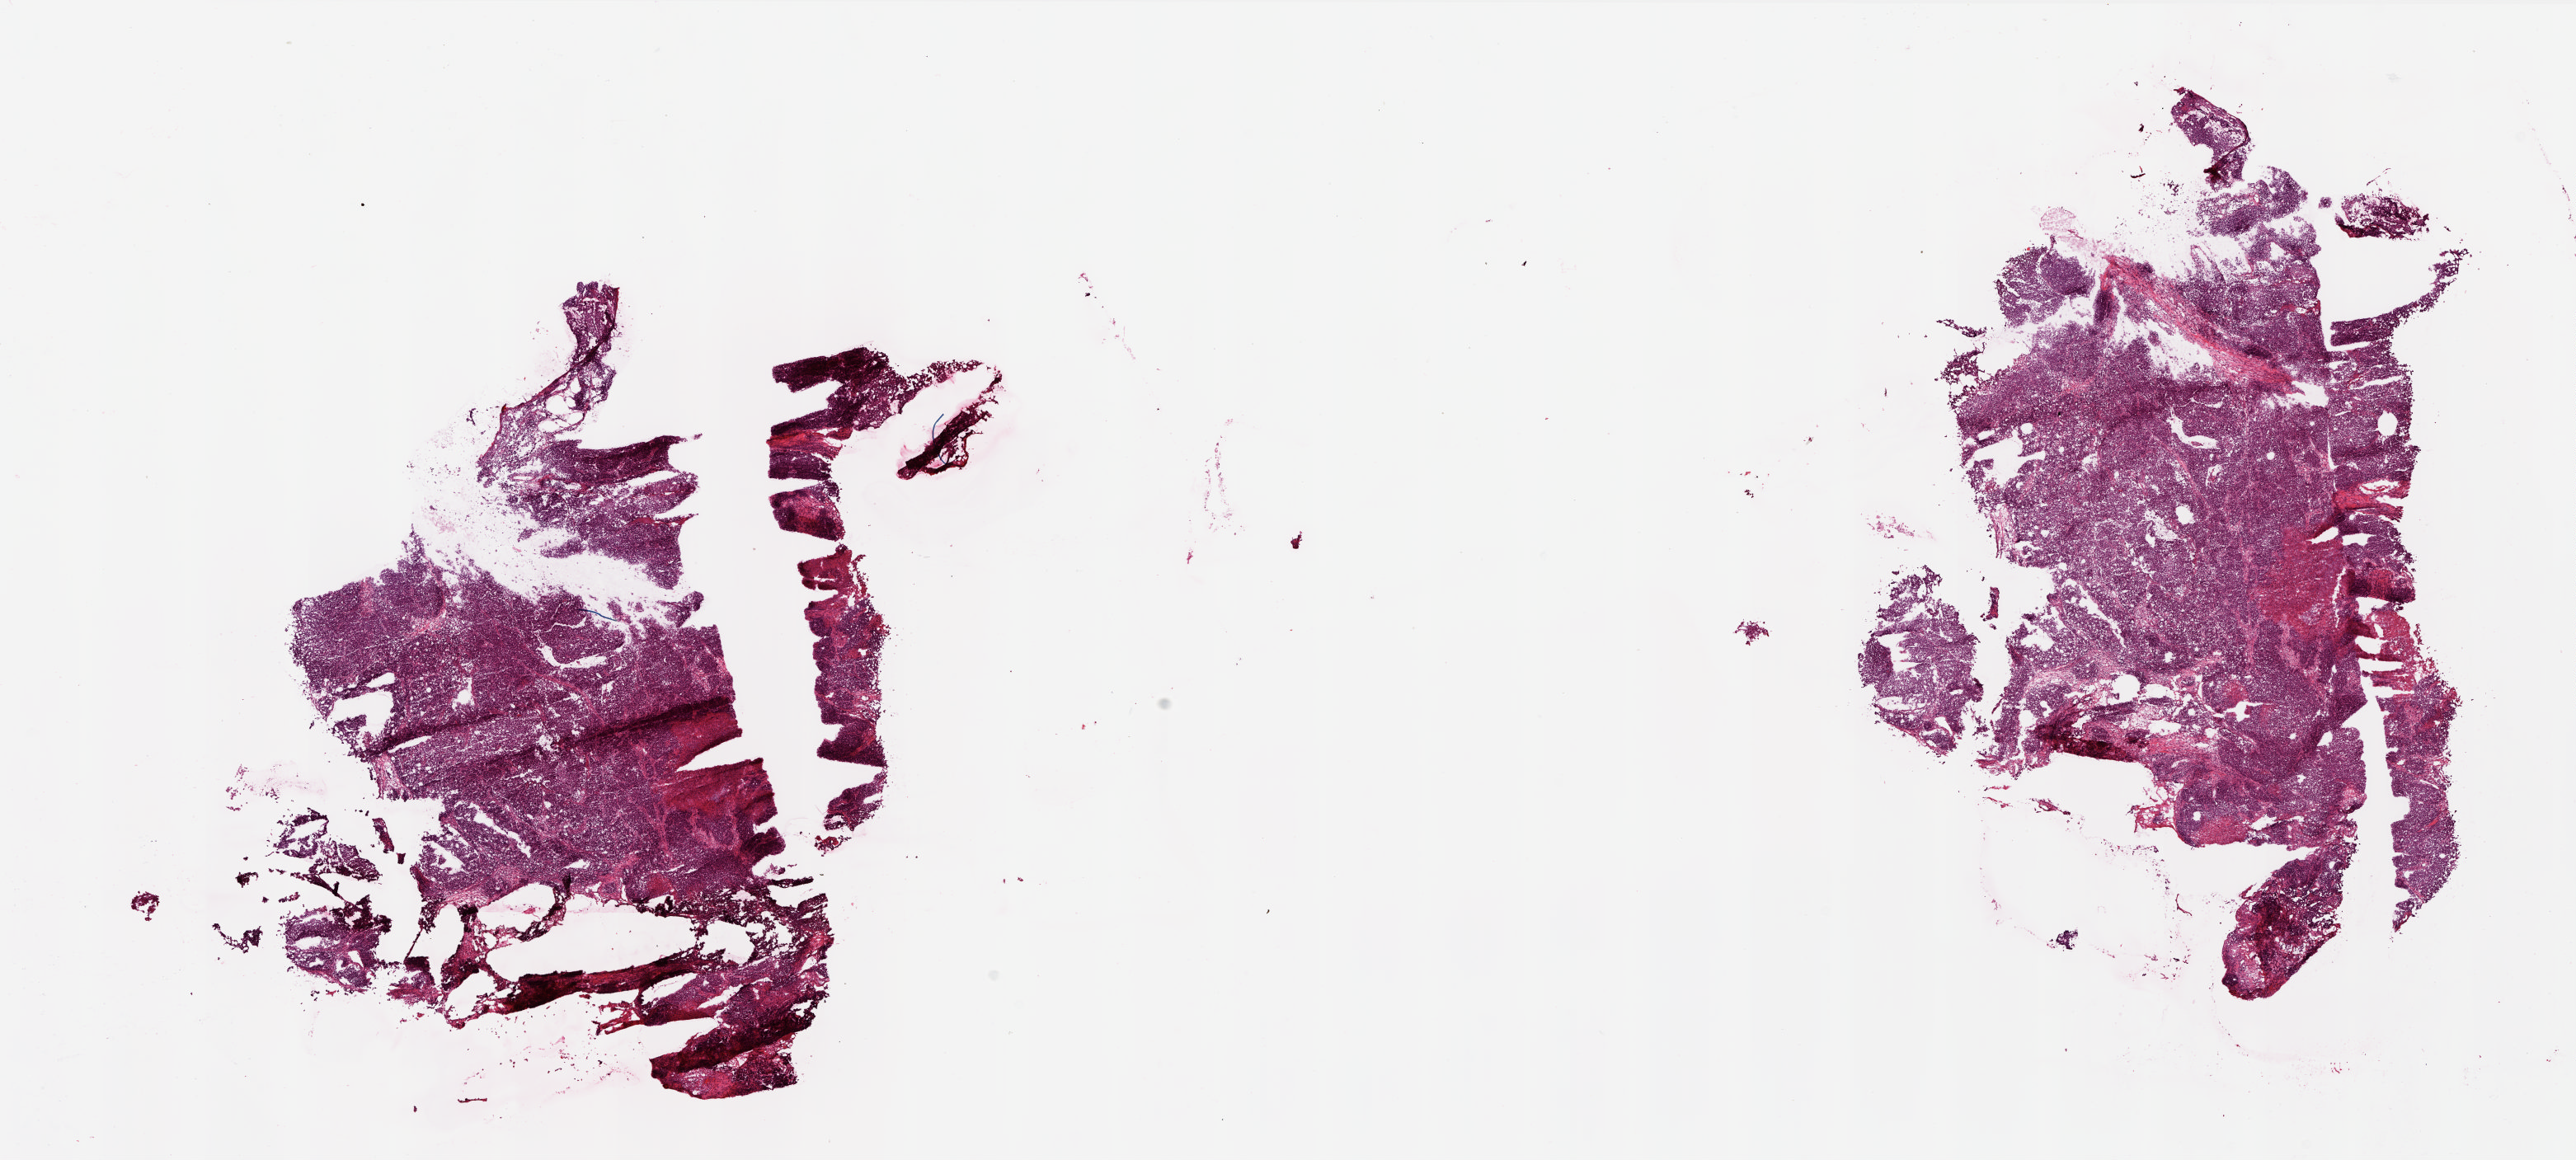
Whole-slide histology image, Hematoxylin and eosin (H&E) stained, a low-resolution overview of the entire scanned area, about 25.0 x 11.2 mm (acquisition: 20x scan), frozen section from the top of the tissue portion, sample: primary tumour, ovary. Female, age 44 years at initial diagnosis.
Diagnosis: Serous cystadenocarcinoma, NOS.